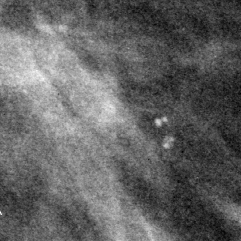
Region of interest cut from a scanned film mammogram (one marked finding), left breast, MLO view, BI-RADS breast density category 2 (scale 1–4).
Calcifications, morphology pleomorphic, distribution regional; BI-RADS assessment category 4; subtlety rating 4 on a 1 (subtle) to 5 (obvious) scale; pathology result (as recorded, not read from the image): benign.